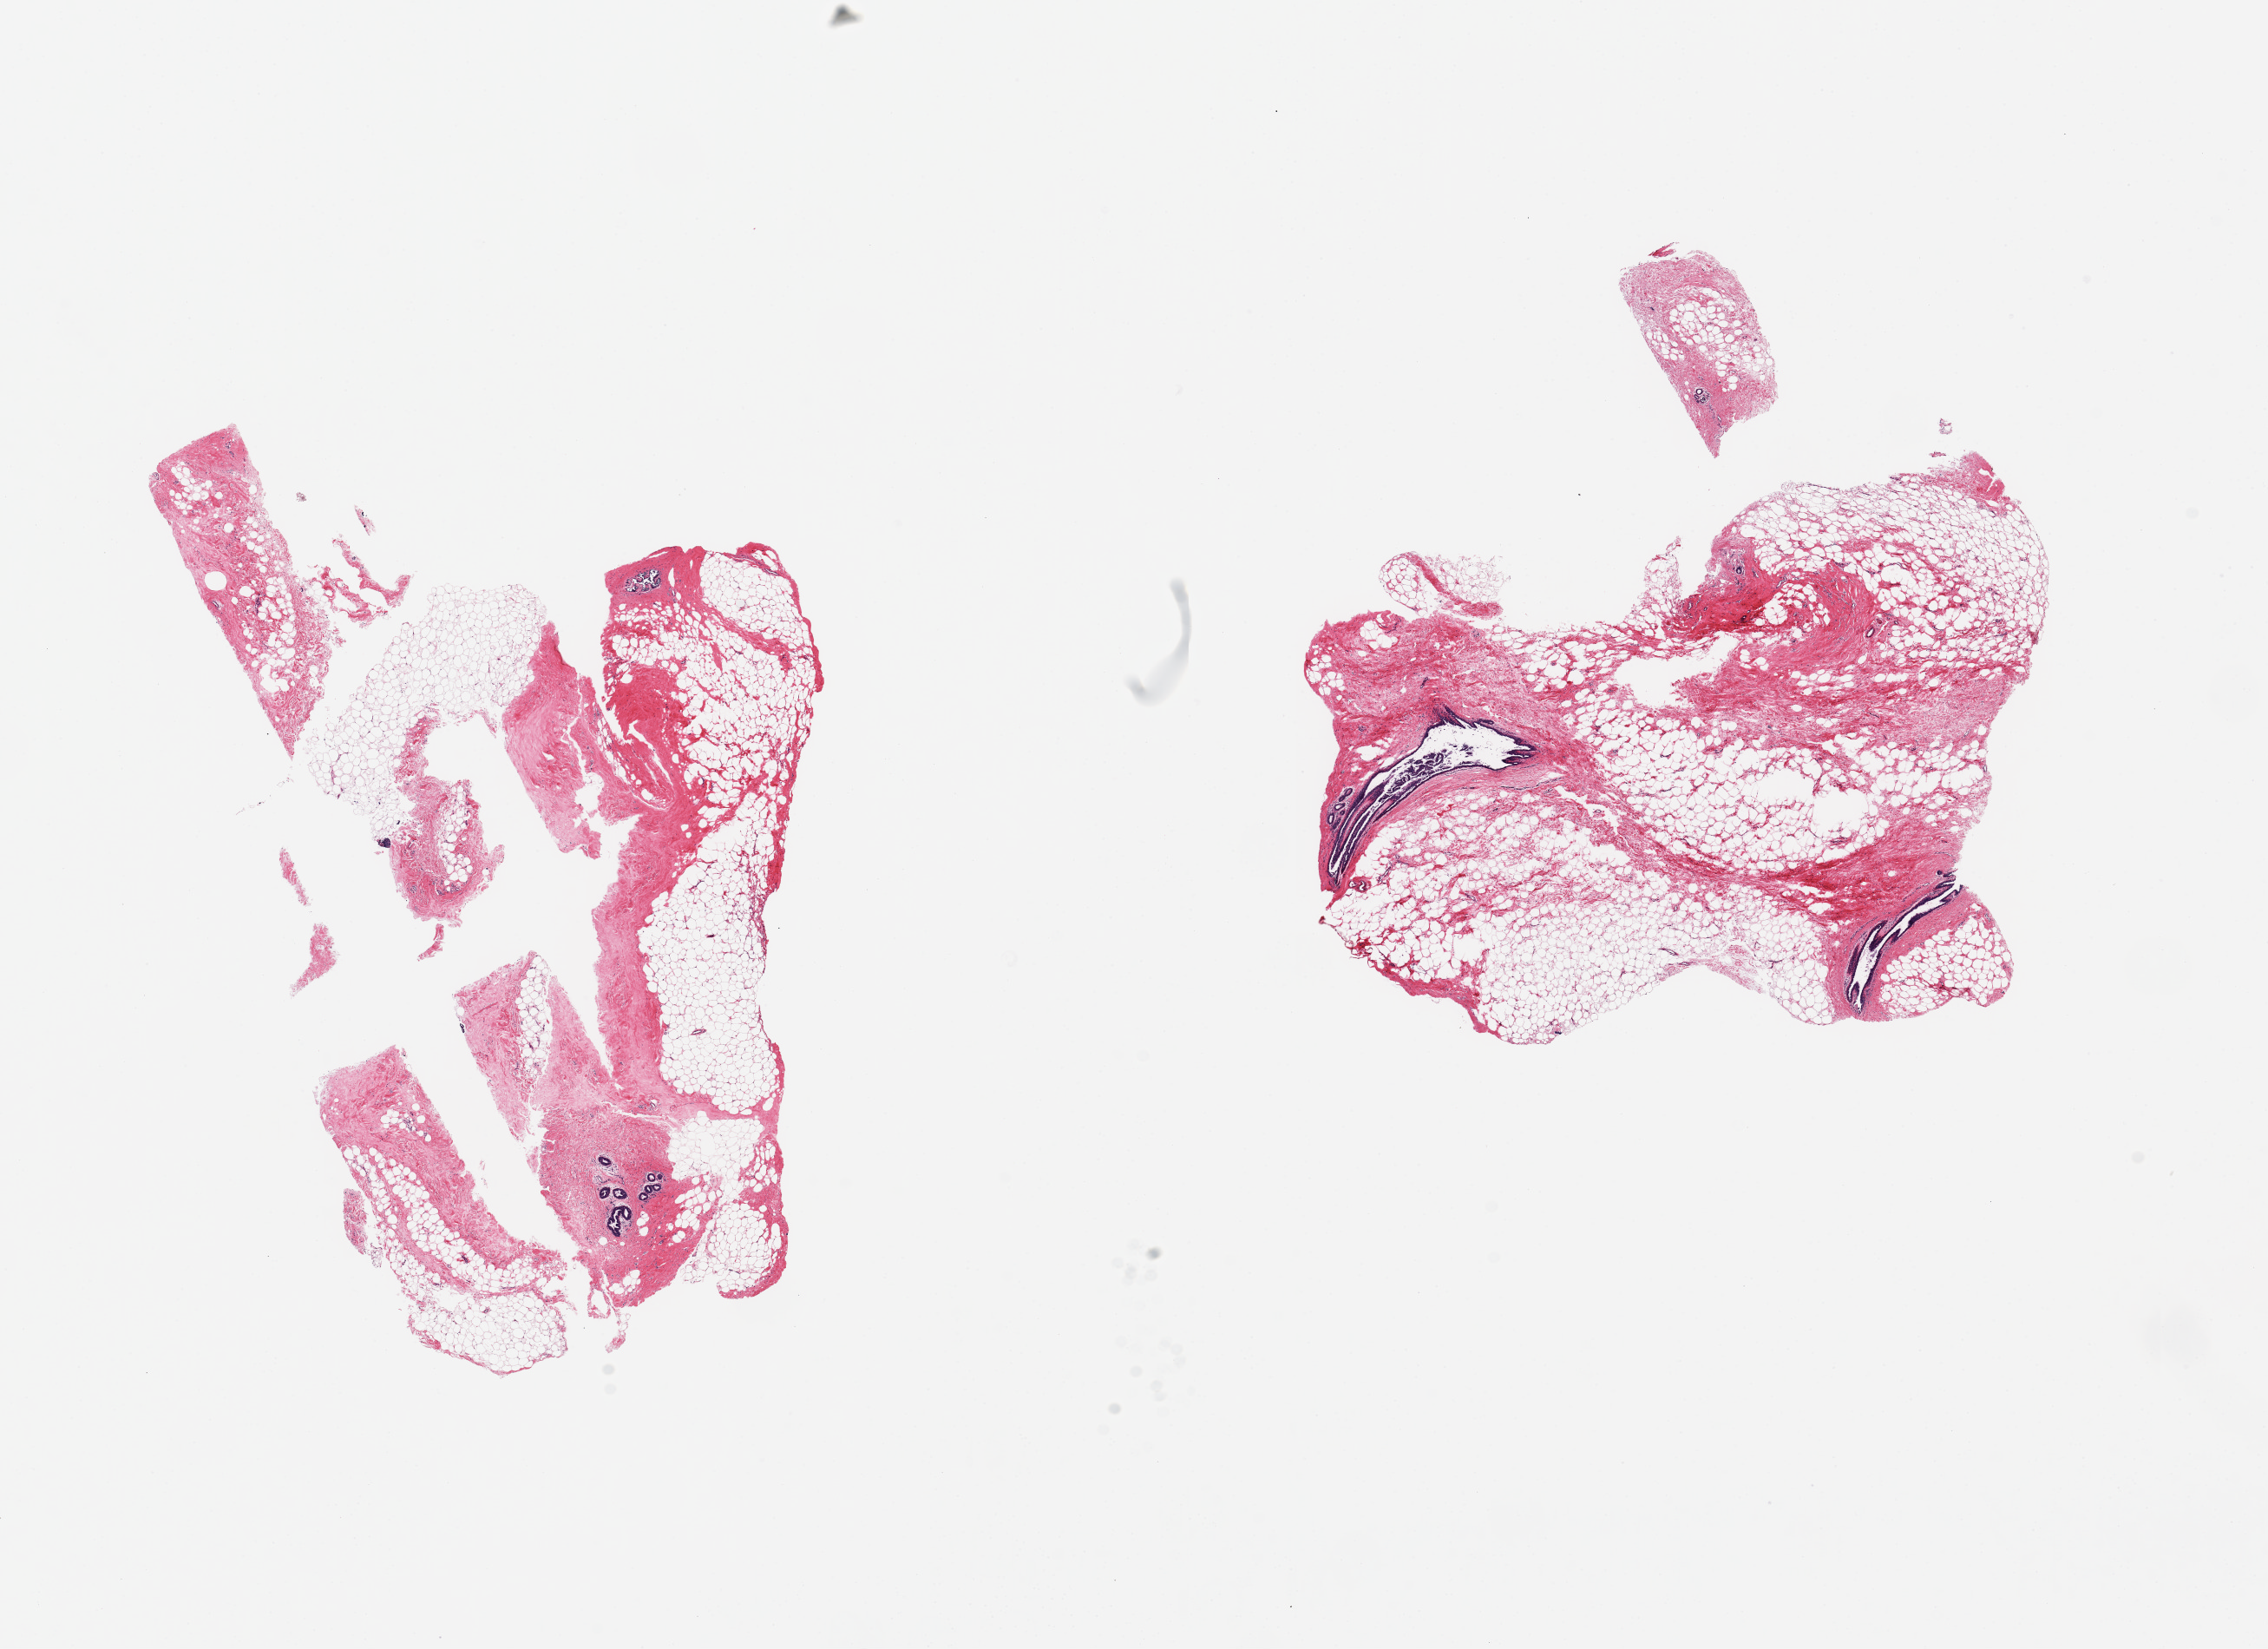
Whole-slide image, haematoxylin and eosin stain, brightfield — whole scanned area (about 20.7 x 15.0 mm, slide scanned at 20x) shown as a low-resolution overview. PAXgene-fixed paraffin-embedded (PFPE) section. Sampled site (target tissue): breast. Tissue donor sample. Donor sex: female.
* pathologist's review note for this sample: 2 pieces, 9x5 & 7x7mm; ducts and immature lobules